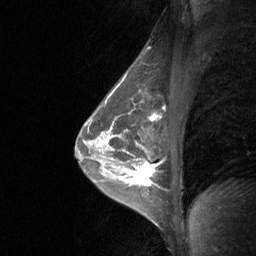
Breast MRI (dynamic contrast-enhanced), one sagittal slice. Position 43 of 64 along the scan axis. Dynamic contrast-enhanced study with each time point stored as its own series, time point 2 of 3 at this slice position (early post-contrast, ordered by acquisition time). 1.5 T. TE 4.8 ms, TR 27 ms. 2 mm slice thickness. 256 × 256 image matrix. Patient: female, 47 years. Case-level facts recorded for this patient, not image findings: setting: breast cancer imaged before/during neoadjuvant chemotherapy; receptor status: HR-positive, HER2-negative.
Annotated regions visible in this slice (semi-automatic segmentation, software-assisted and operator-edited):
- analysis volume of interest (the breast-tissue region the enhancement analysis was run in; not a lesion): bounding box [x1, y1, x2, y2] px = [120, 142, 156, 203]
- tumour enhancement mask (voxels above the 90 % enhancement threshold inside the analysis volume of interest): [135, 163, 153, 185]